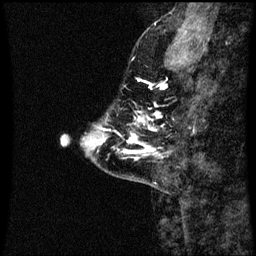
Breast MRI (dynamic contrast-enhanced), one sagittal slice; position 12 of 60 along the scan axis; dynamic contrast-enhanced series, image 2 of 3 at this slice position (ordered by acquisition); 1.5 T; TE 4.2 ms, TR 8.9 ms; 256 × 256 image matrix. Female patient, age 43 years. From the clinical record (not read from this slice): setting: breast cancer imaged before/during neoadjuvant chemotherapy; receptor status: HR-positive, HER2-negative.
Outlined on this slice (semi-automatically segmented with operator editing):
- analysis volume of interest (the breast-tissue region the enhancement analysis was run in; not a lesion): bounding box <115,102,163,161> (left, top, right, bottom; pixels)
- tumour enhancement mask (voxels above the 70 % enhancement threshold inside the analysis volume of interest): <124,114,160,159>